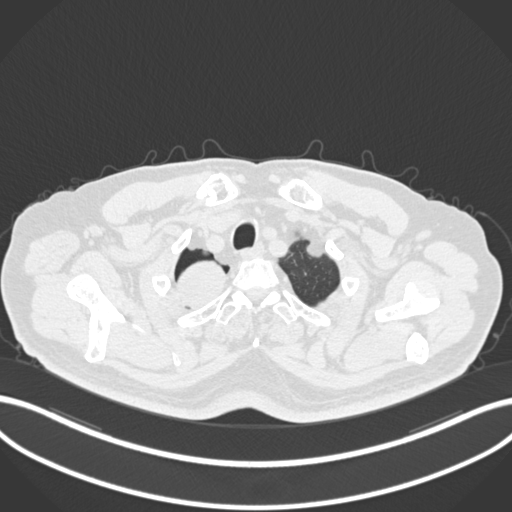
Chest CT, one axial slice; slice 197 of 218 in the series (ordered by position); reconstruction kernel B30f; 120 kVp; lung window (W 1500 / L -600 HU); 512 × 512 image matrix, field of view 400 × 400 mm. Patient: male, 68 years. Case-level facts recorded for this patient, not image findings: clinical TNM (as recorded): T2a N0 M0.
Outlined on this slice (bounding box drawn by a radiologist):
- lung tumour (recorded histology: adenocarcinoma): bounding box <172,257,231,314> (left, top, right, bottom; pixels)